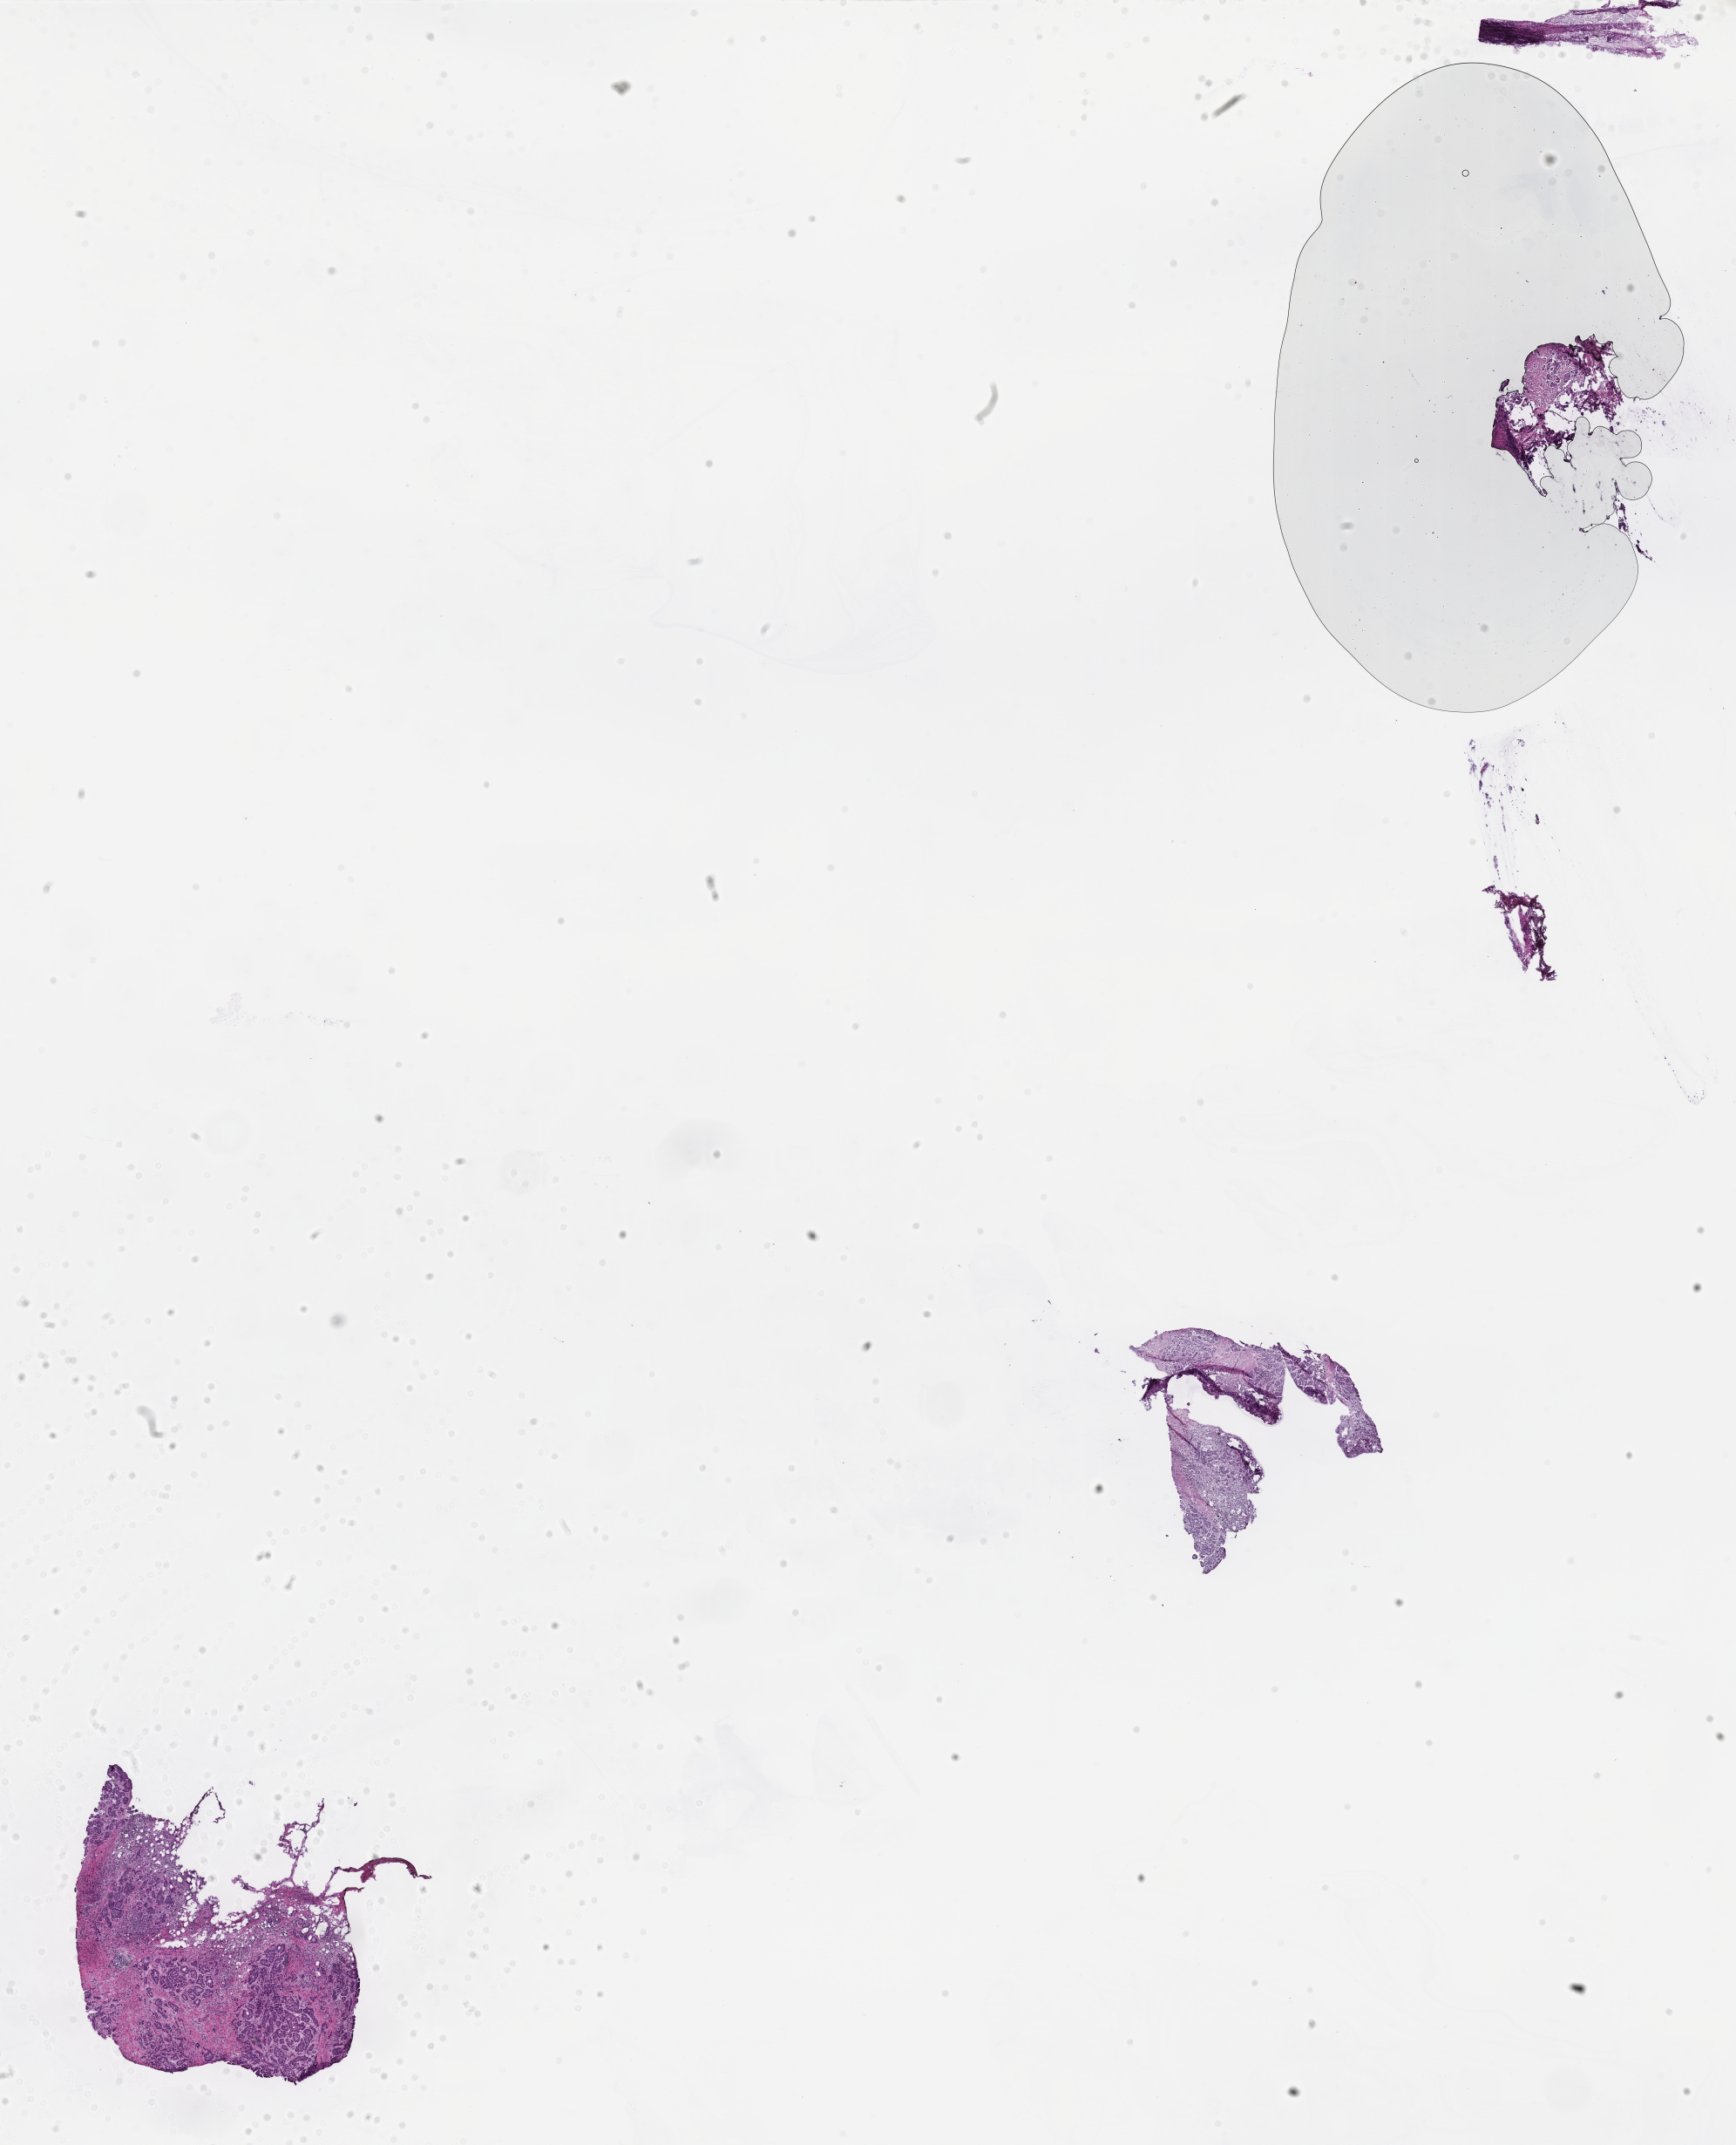
Hematoxylin and eosin (H&E) whole-slide image, whole scanned area (about 16.1 x 19.9 mm) shown as a low-resolution overview; frozen section (tissue freezing medium); specimen: primary tumor; anatomic site: breast. Female, age 79 years at initial diagnosis.
Histologic diagnosis: Infiltrating duct carcinoma, NOS.